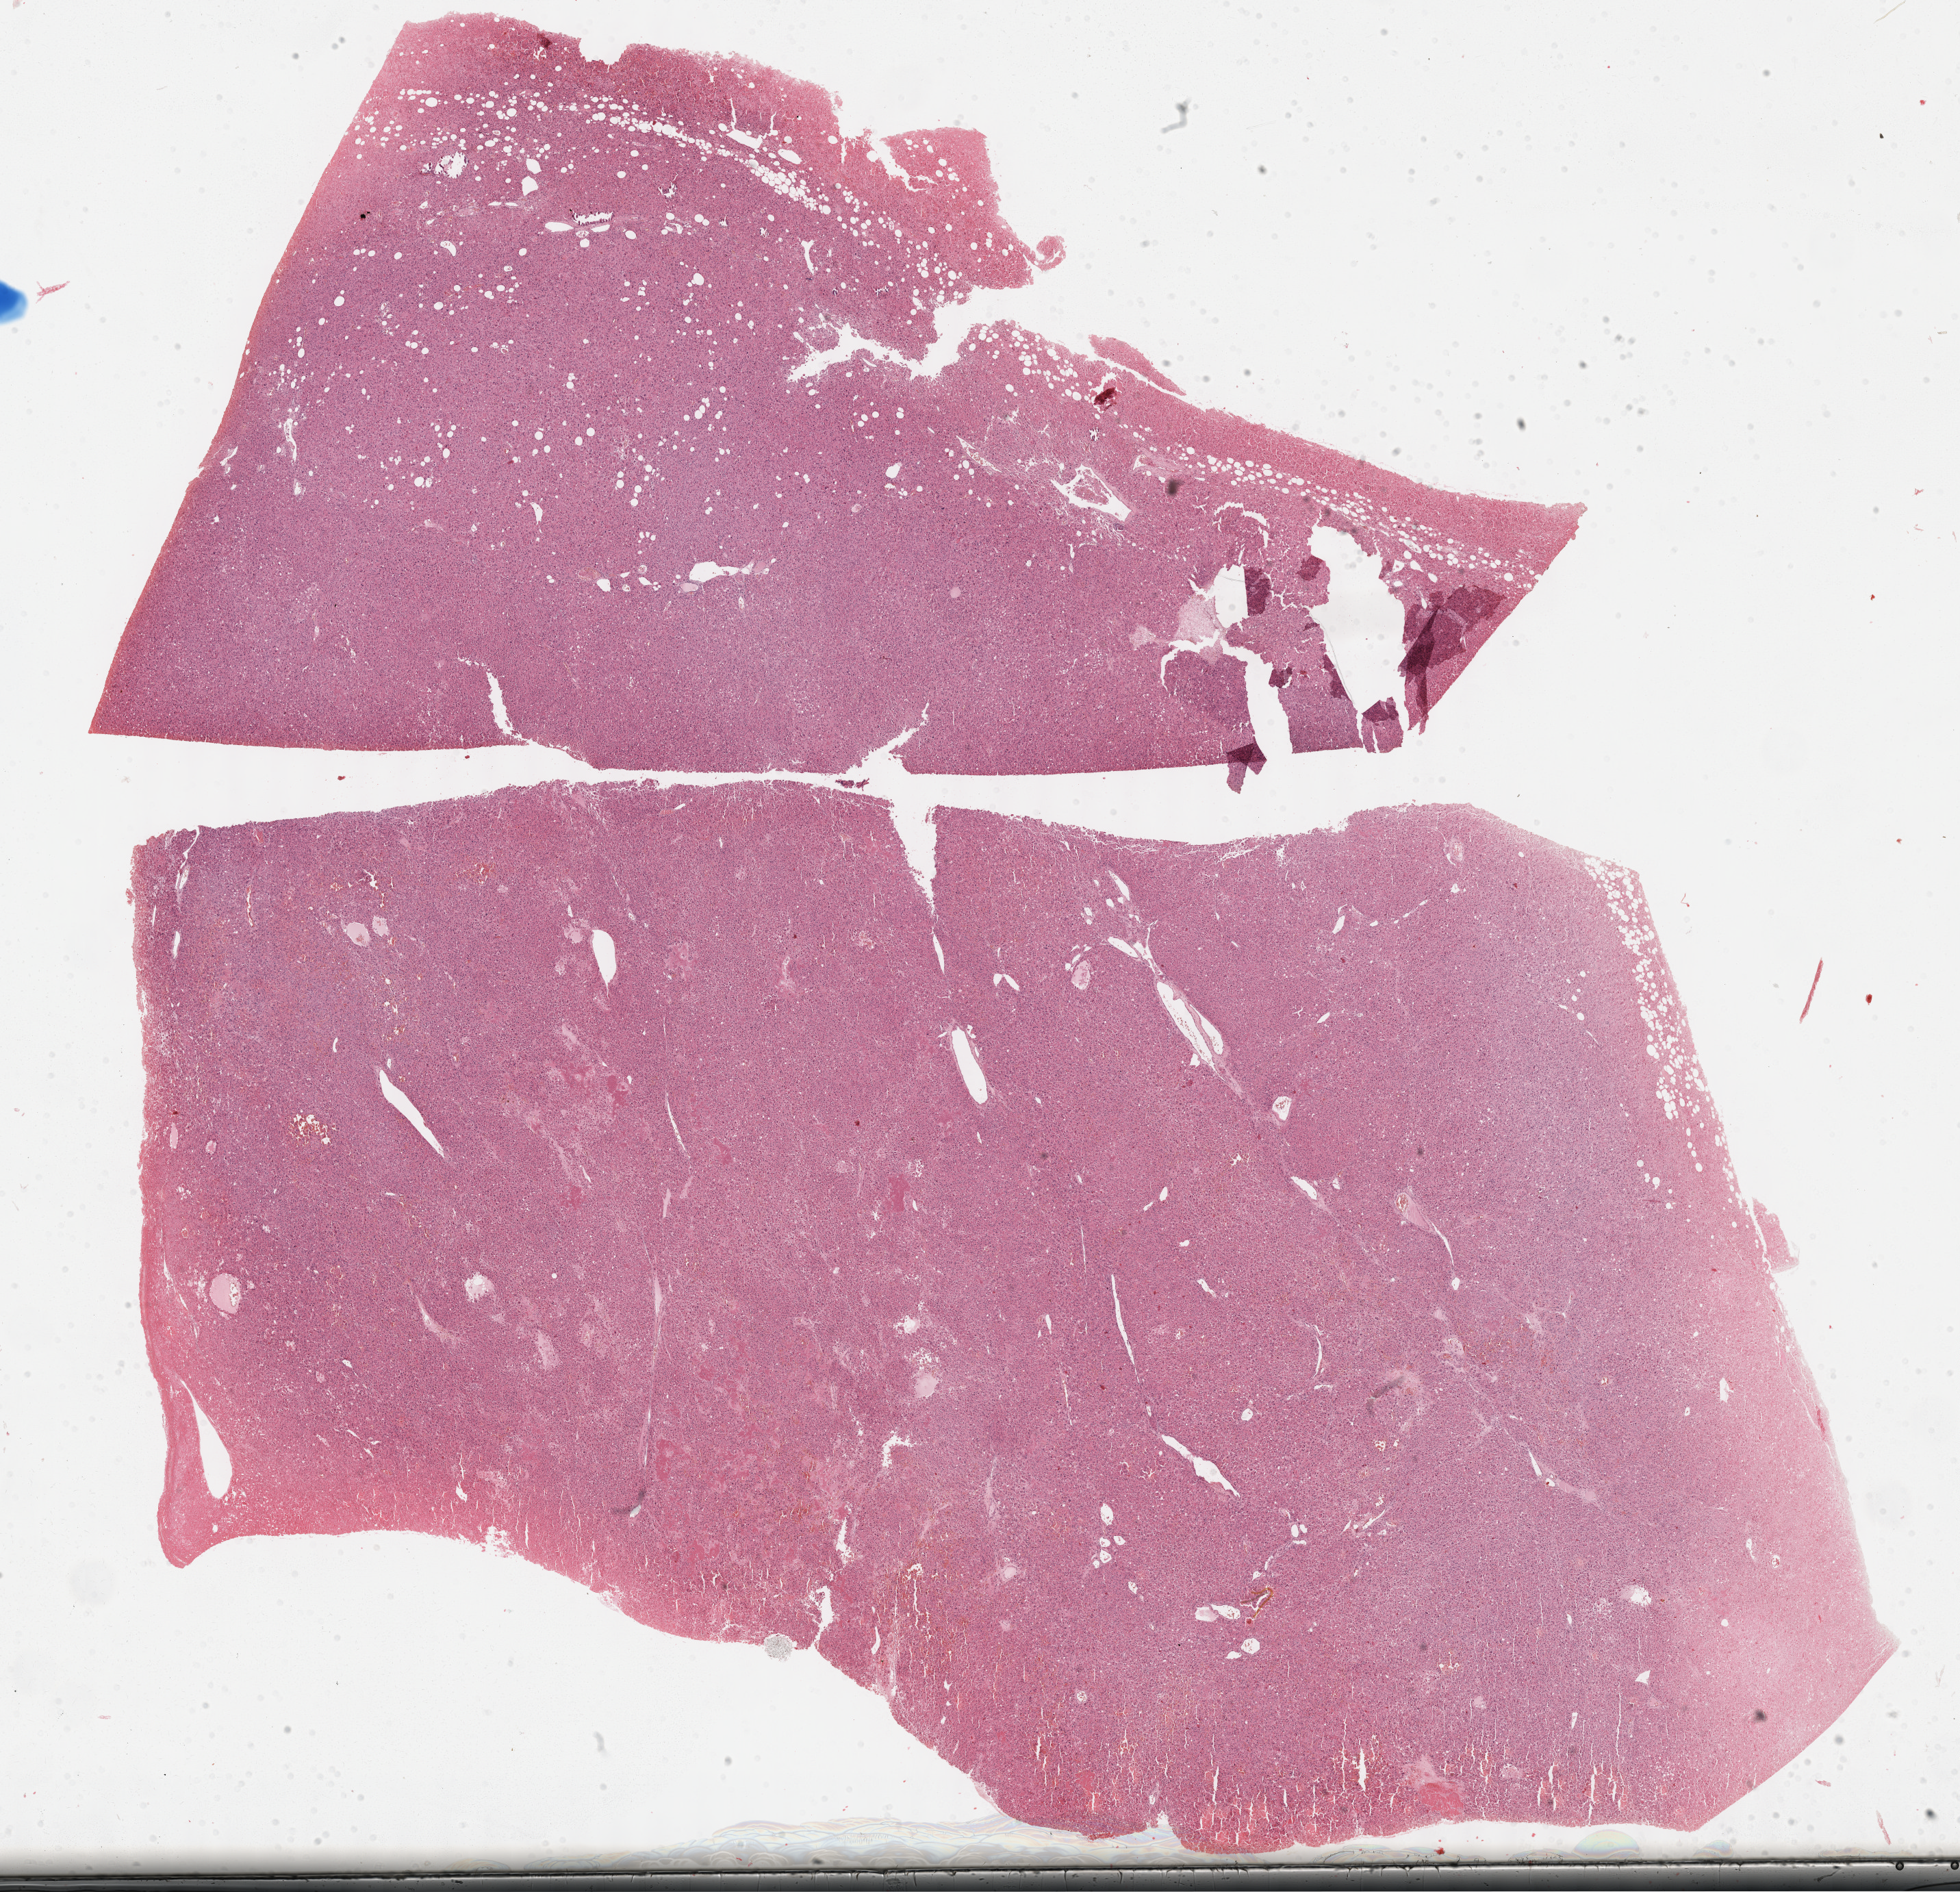
Digitized H&E-stained tissue section (whole slide) — whole scanned area (about 23.2 x 22.3 mm, from a 40x scan) shown as a low-resolution overview. FFPE section. Adrenal cortex, primary tumour sample. Patient: female, age at initial diagnosis 29 years.
Pathologic diagnosis: Adrenal cortical carcinoma (cortex of adrenal gland).